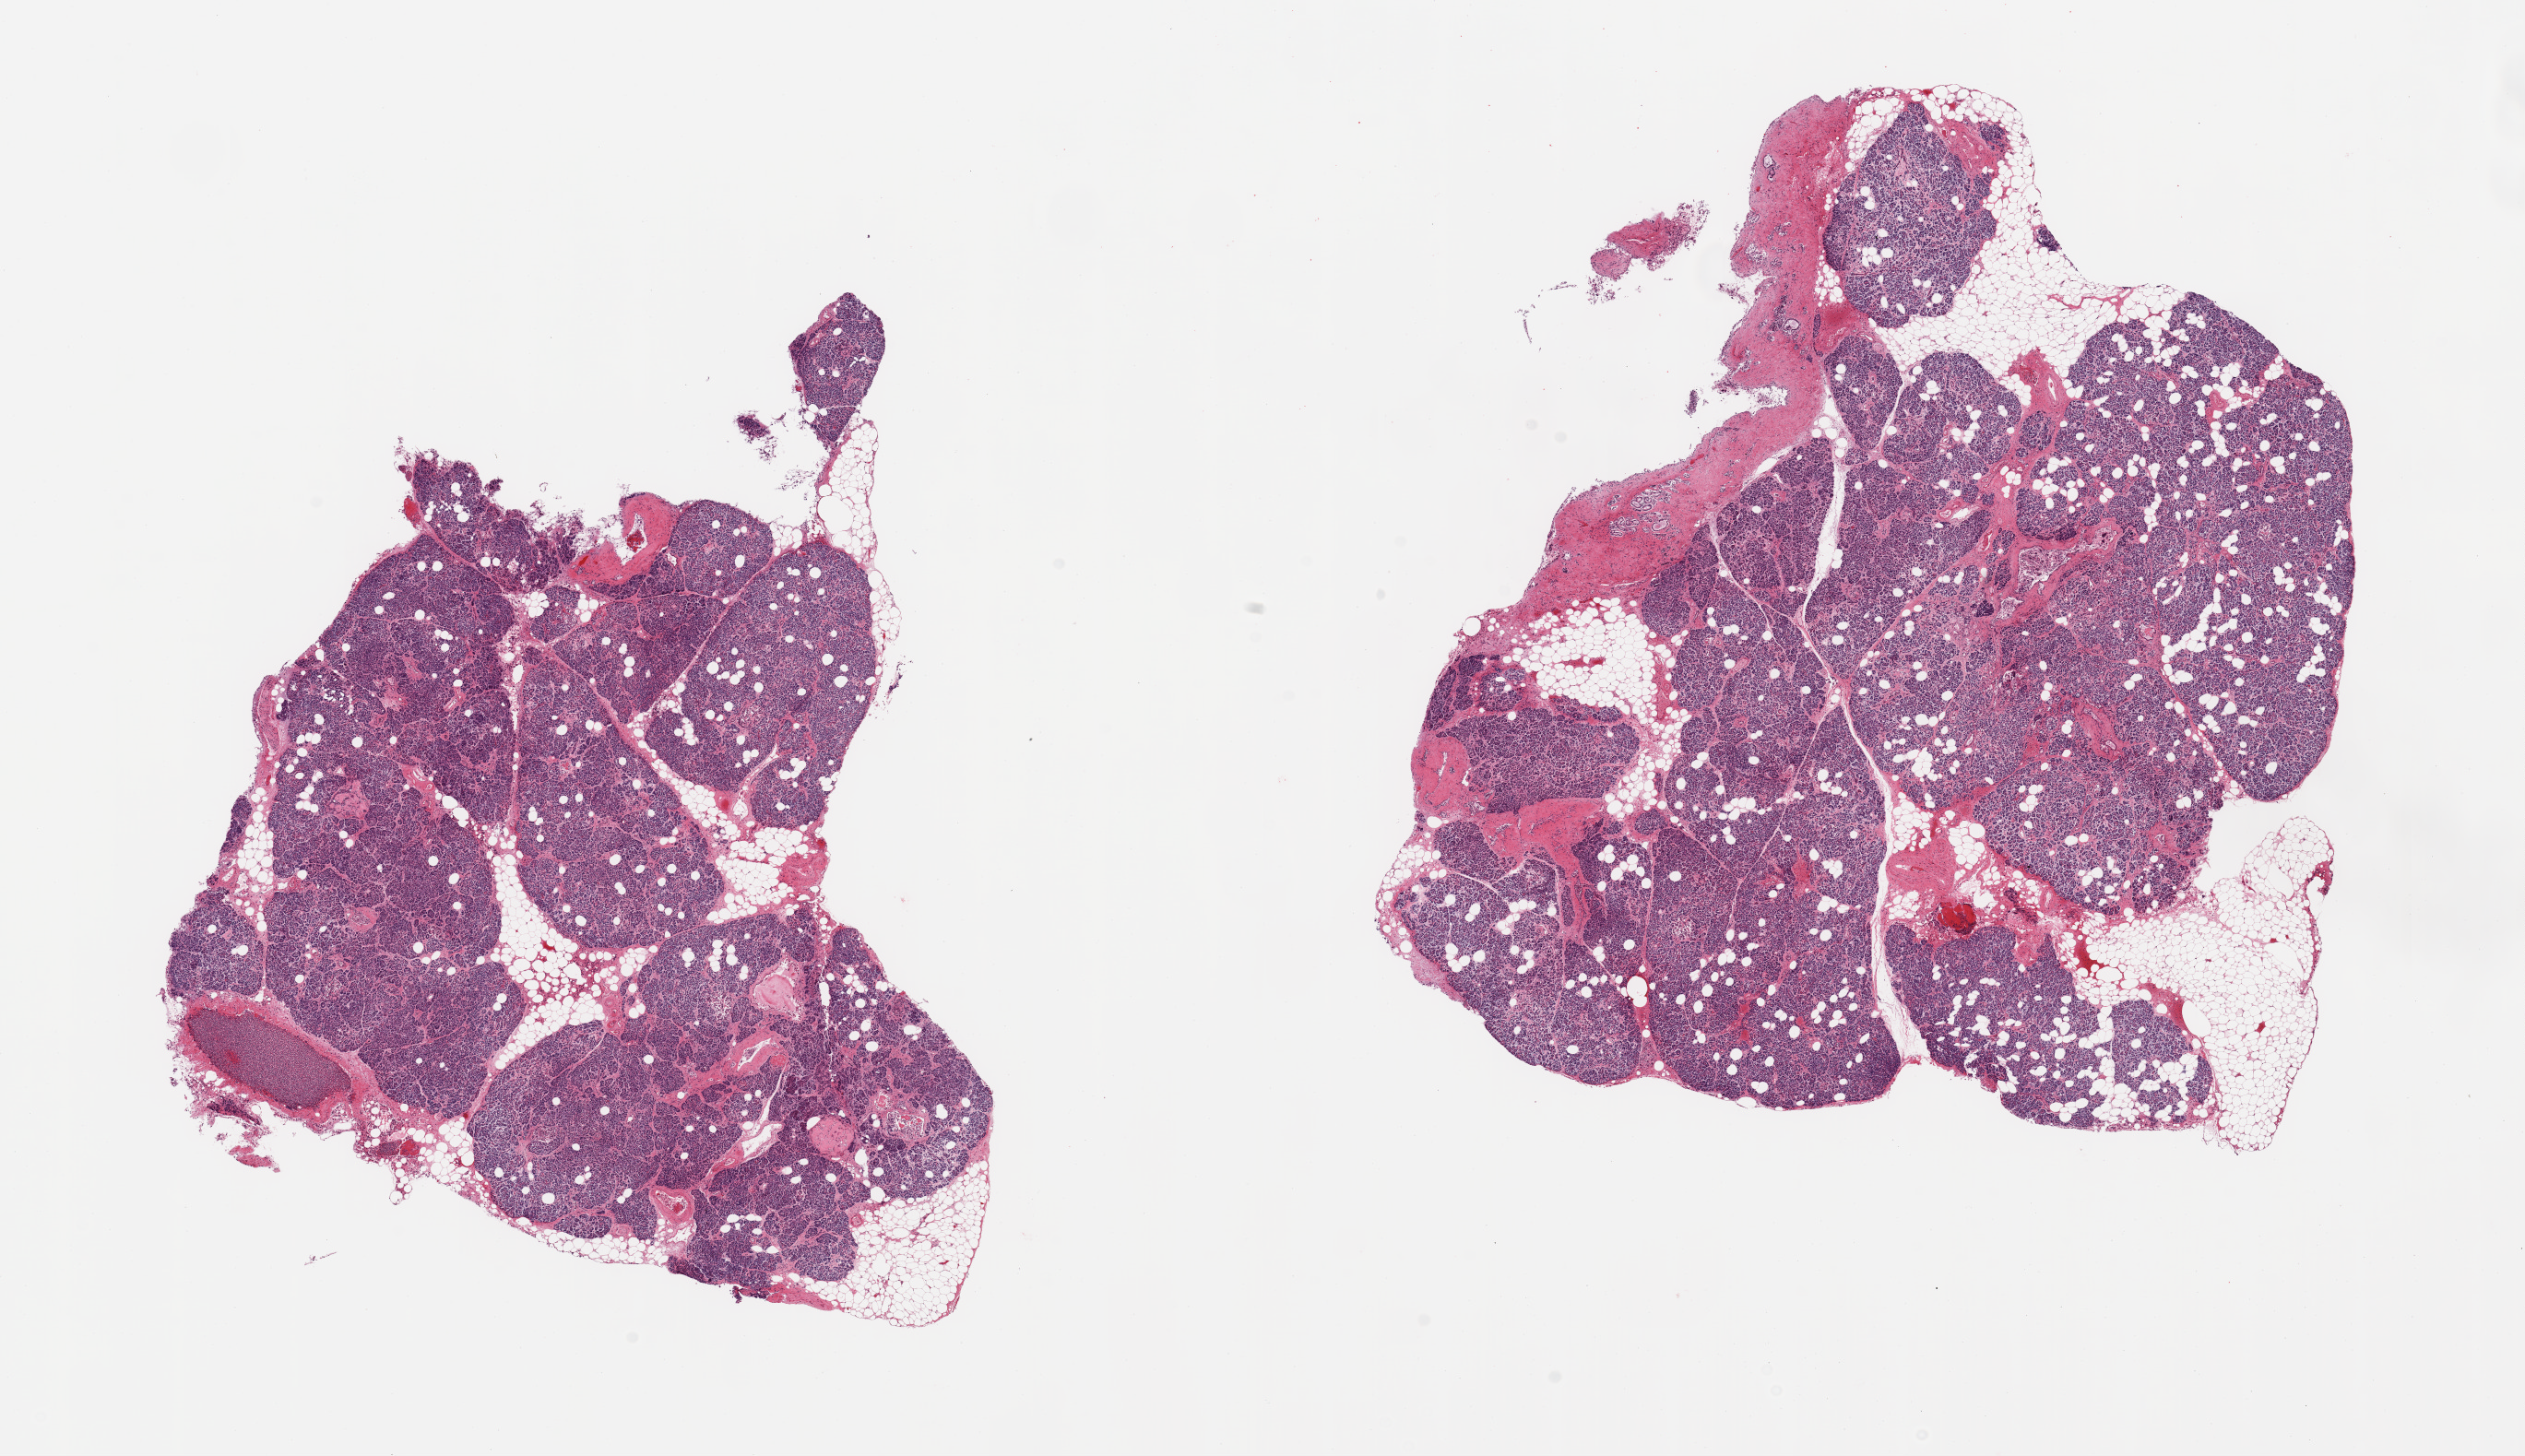
Whole-slide image, H&E stain, brightfield, shown as a low-resolution overview of the whole scanned area (about 21.7 x 12.5 mm, slide scanned at 20x). PAXgene-fixed, paraffin-embedded tissue. Target tissue: pancreas. Tissue donor sample. Female donor.
- reviewer comment on this tissue sample: 2 pieces, moderately advanced saponfication, Islets poorly preserved, one degenerating exampled